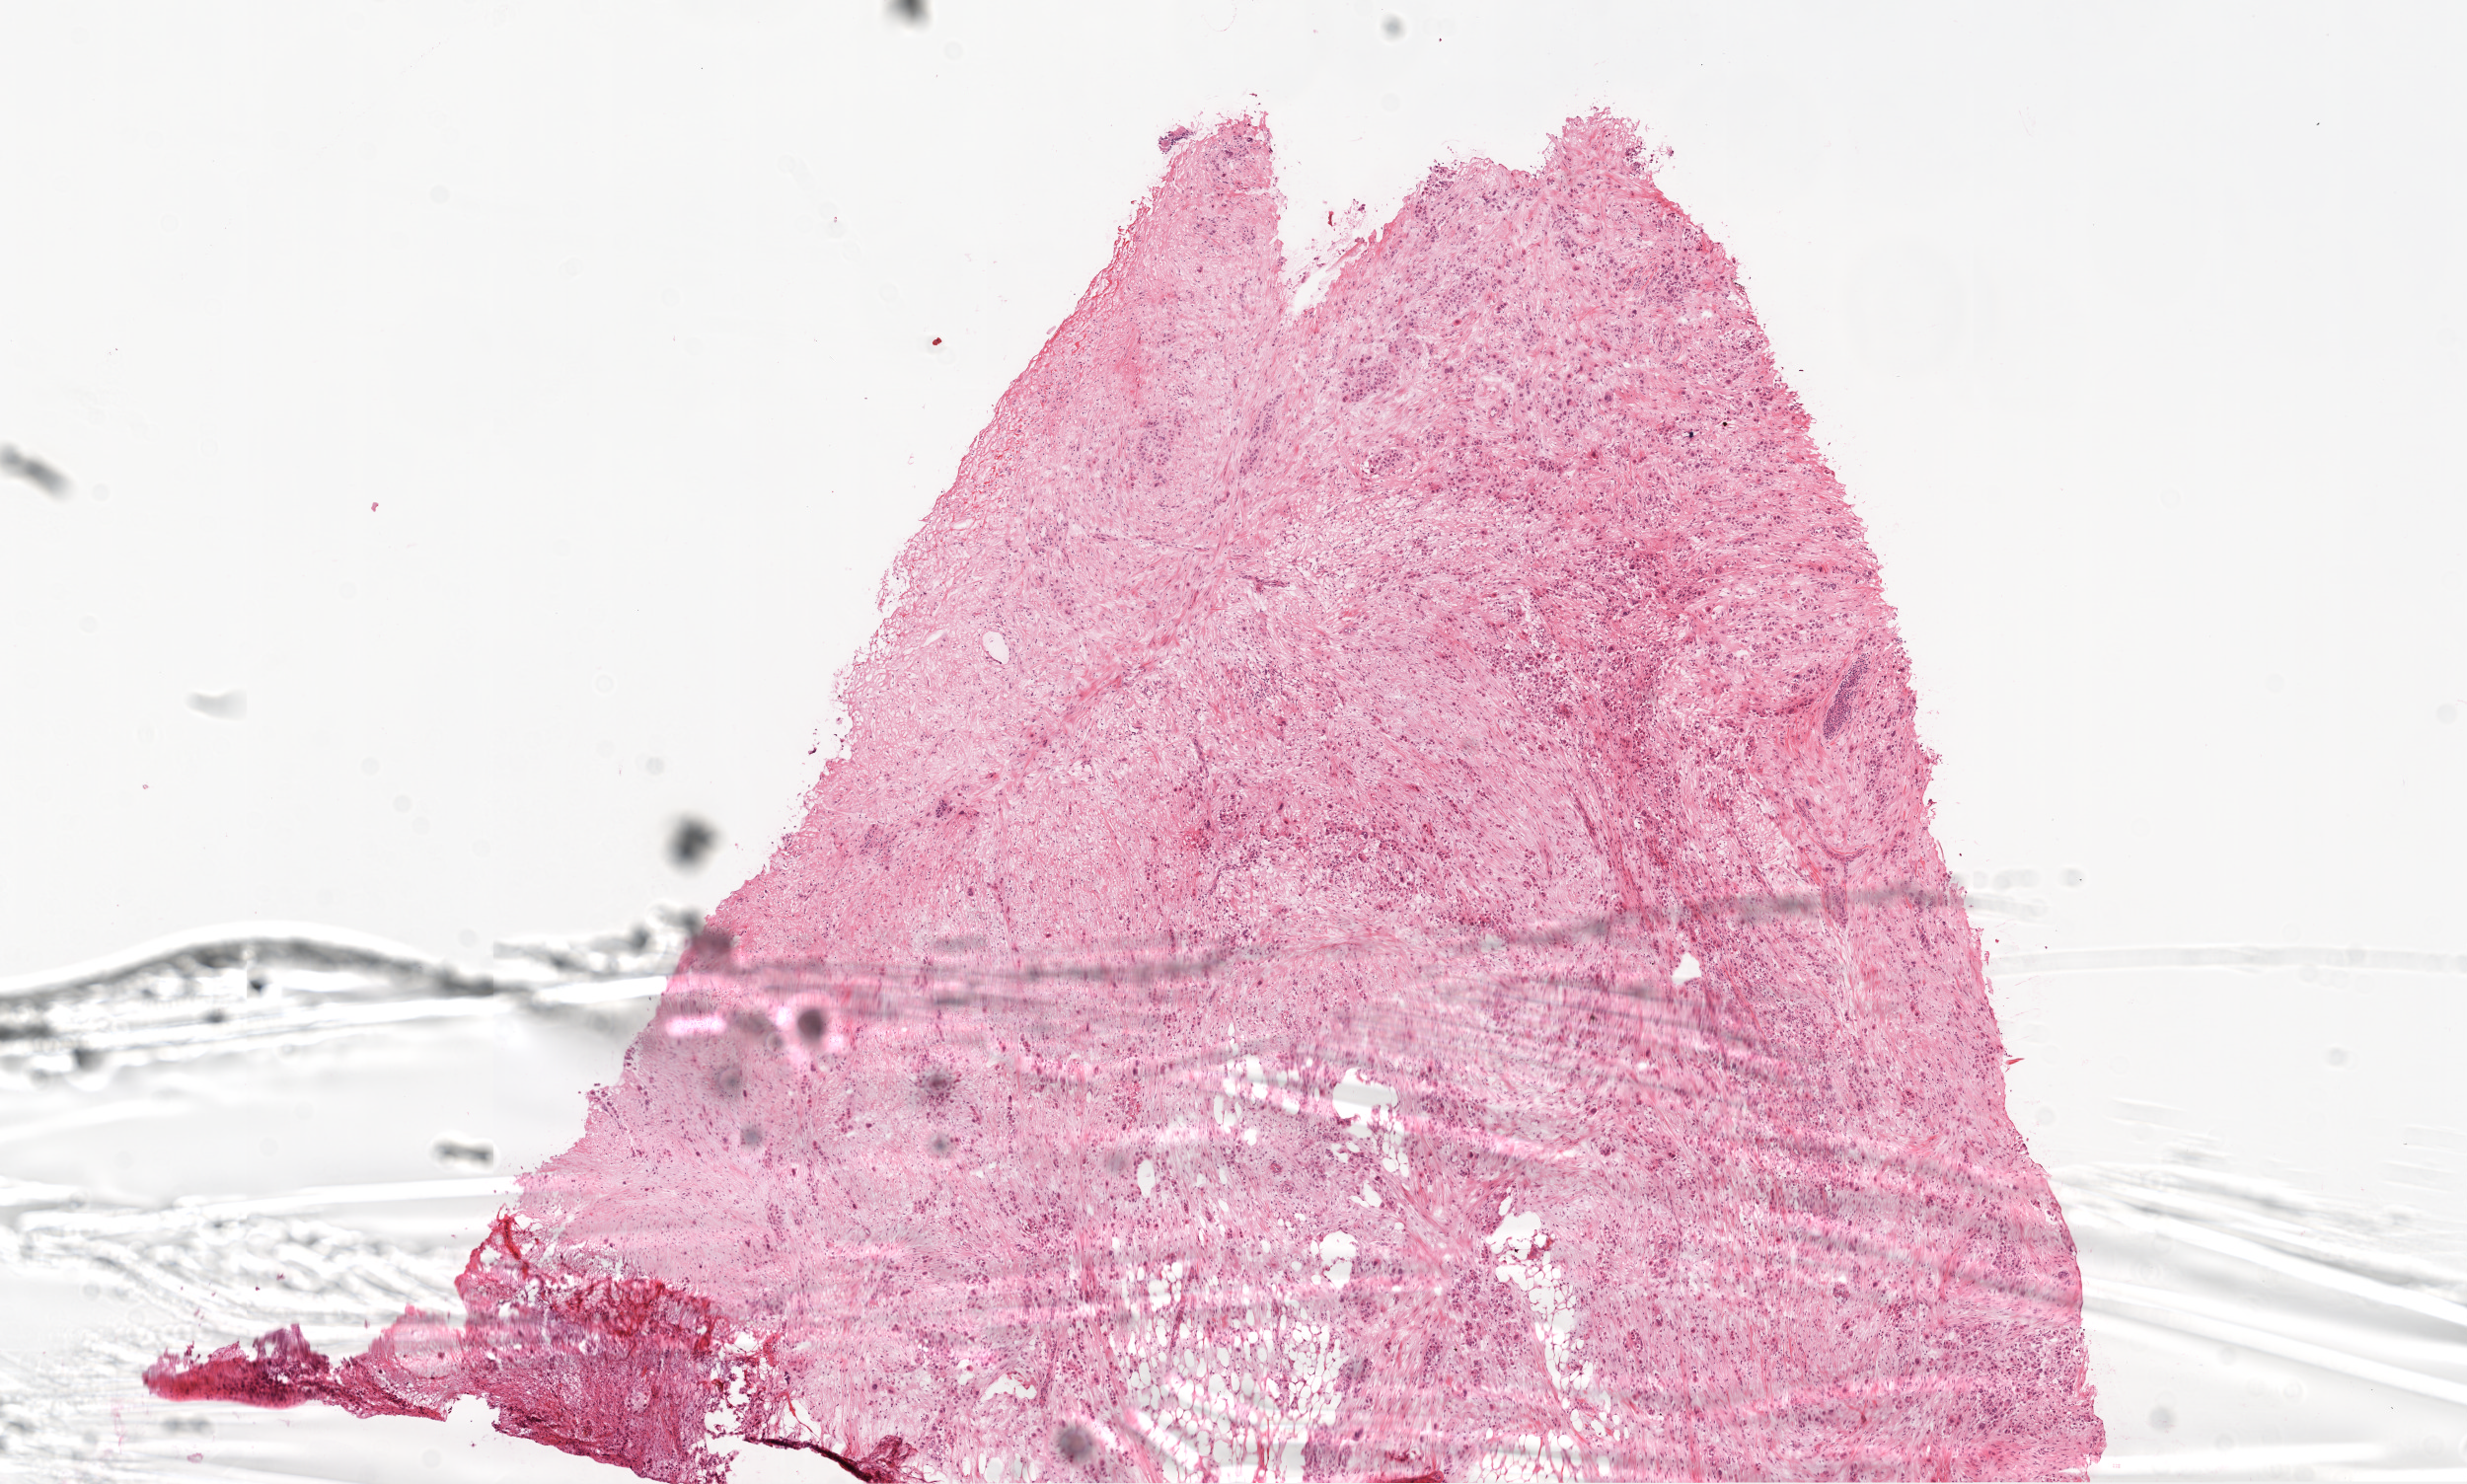
Whole-slide histology image, H&E — shown as a low-resolution overview of the whole scanned area (about 10.0 x 6.0 mm), frozen section, ovary, recurrent tumour sample. Female patient; age at initial diagnosis 40 years. Pathologist review of this section (percent, as recorded): tumour cells 20%, tumour nuclei 70%, normal cells 0%, stromal cells 80%, necrosis 0%.
• this section: recurrent tumour
• patient diagnosis: Serous cystadenocarcinoma, NOS